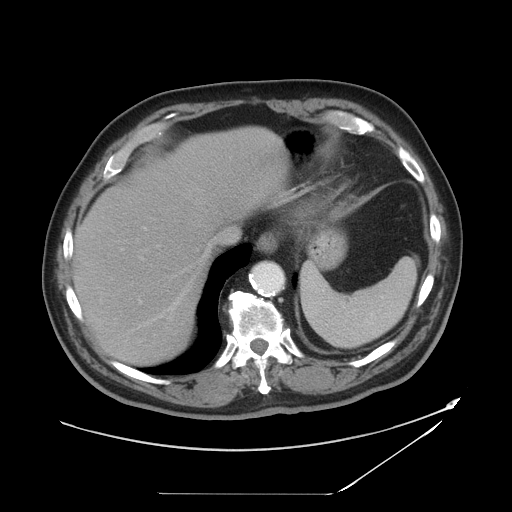
Contrast-enhanced abdominal CT, one axial slice. Position 37 of 49 along the scan axis. 120 kVp. Intravenous contrast given. Soft-tissue window (W 400 / L 40 HU). 5 mm slice thickness. 512 × 512 image matrix, field of view 461 × 461 mm. Male patient, age 72 years. Case-level facts recorded for this patient, not image findings: diagnosis: colorectal cancer liver metastases, imaged before liver resection; multiple liver metastases: no; largest metastasis: 2.5 cm.
Annotated regions visible in this slice (manually delineated by an expert):
- hepatic veins: bounding box (x1, y1, x2, y2) in pixels: (144, 238, 216, 326)
- liver: (78, 128, 283, 363)
- planned liver remnant (the part of the liver to remain after resection): (78, 182, 210, 362)